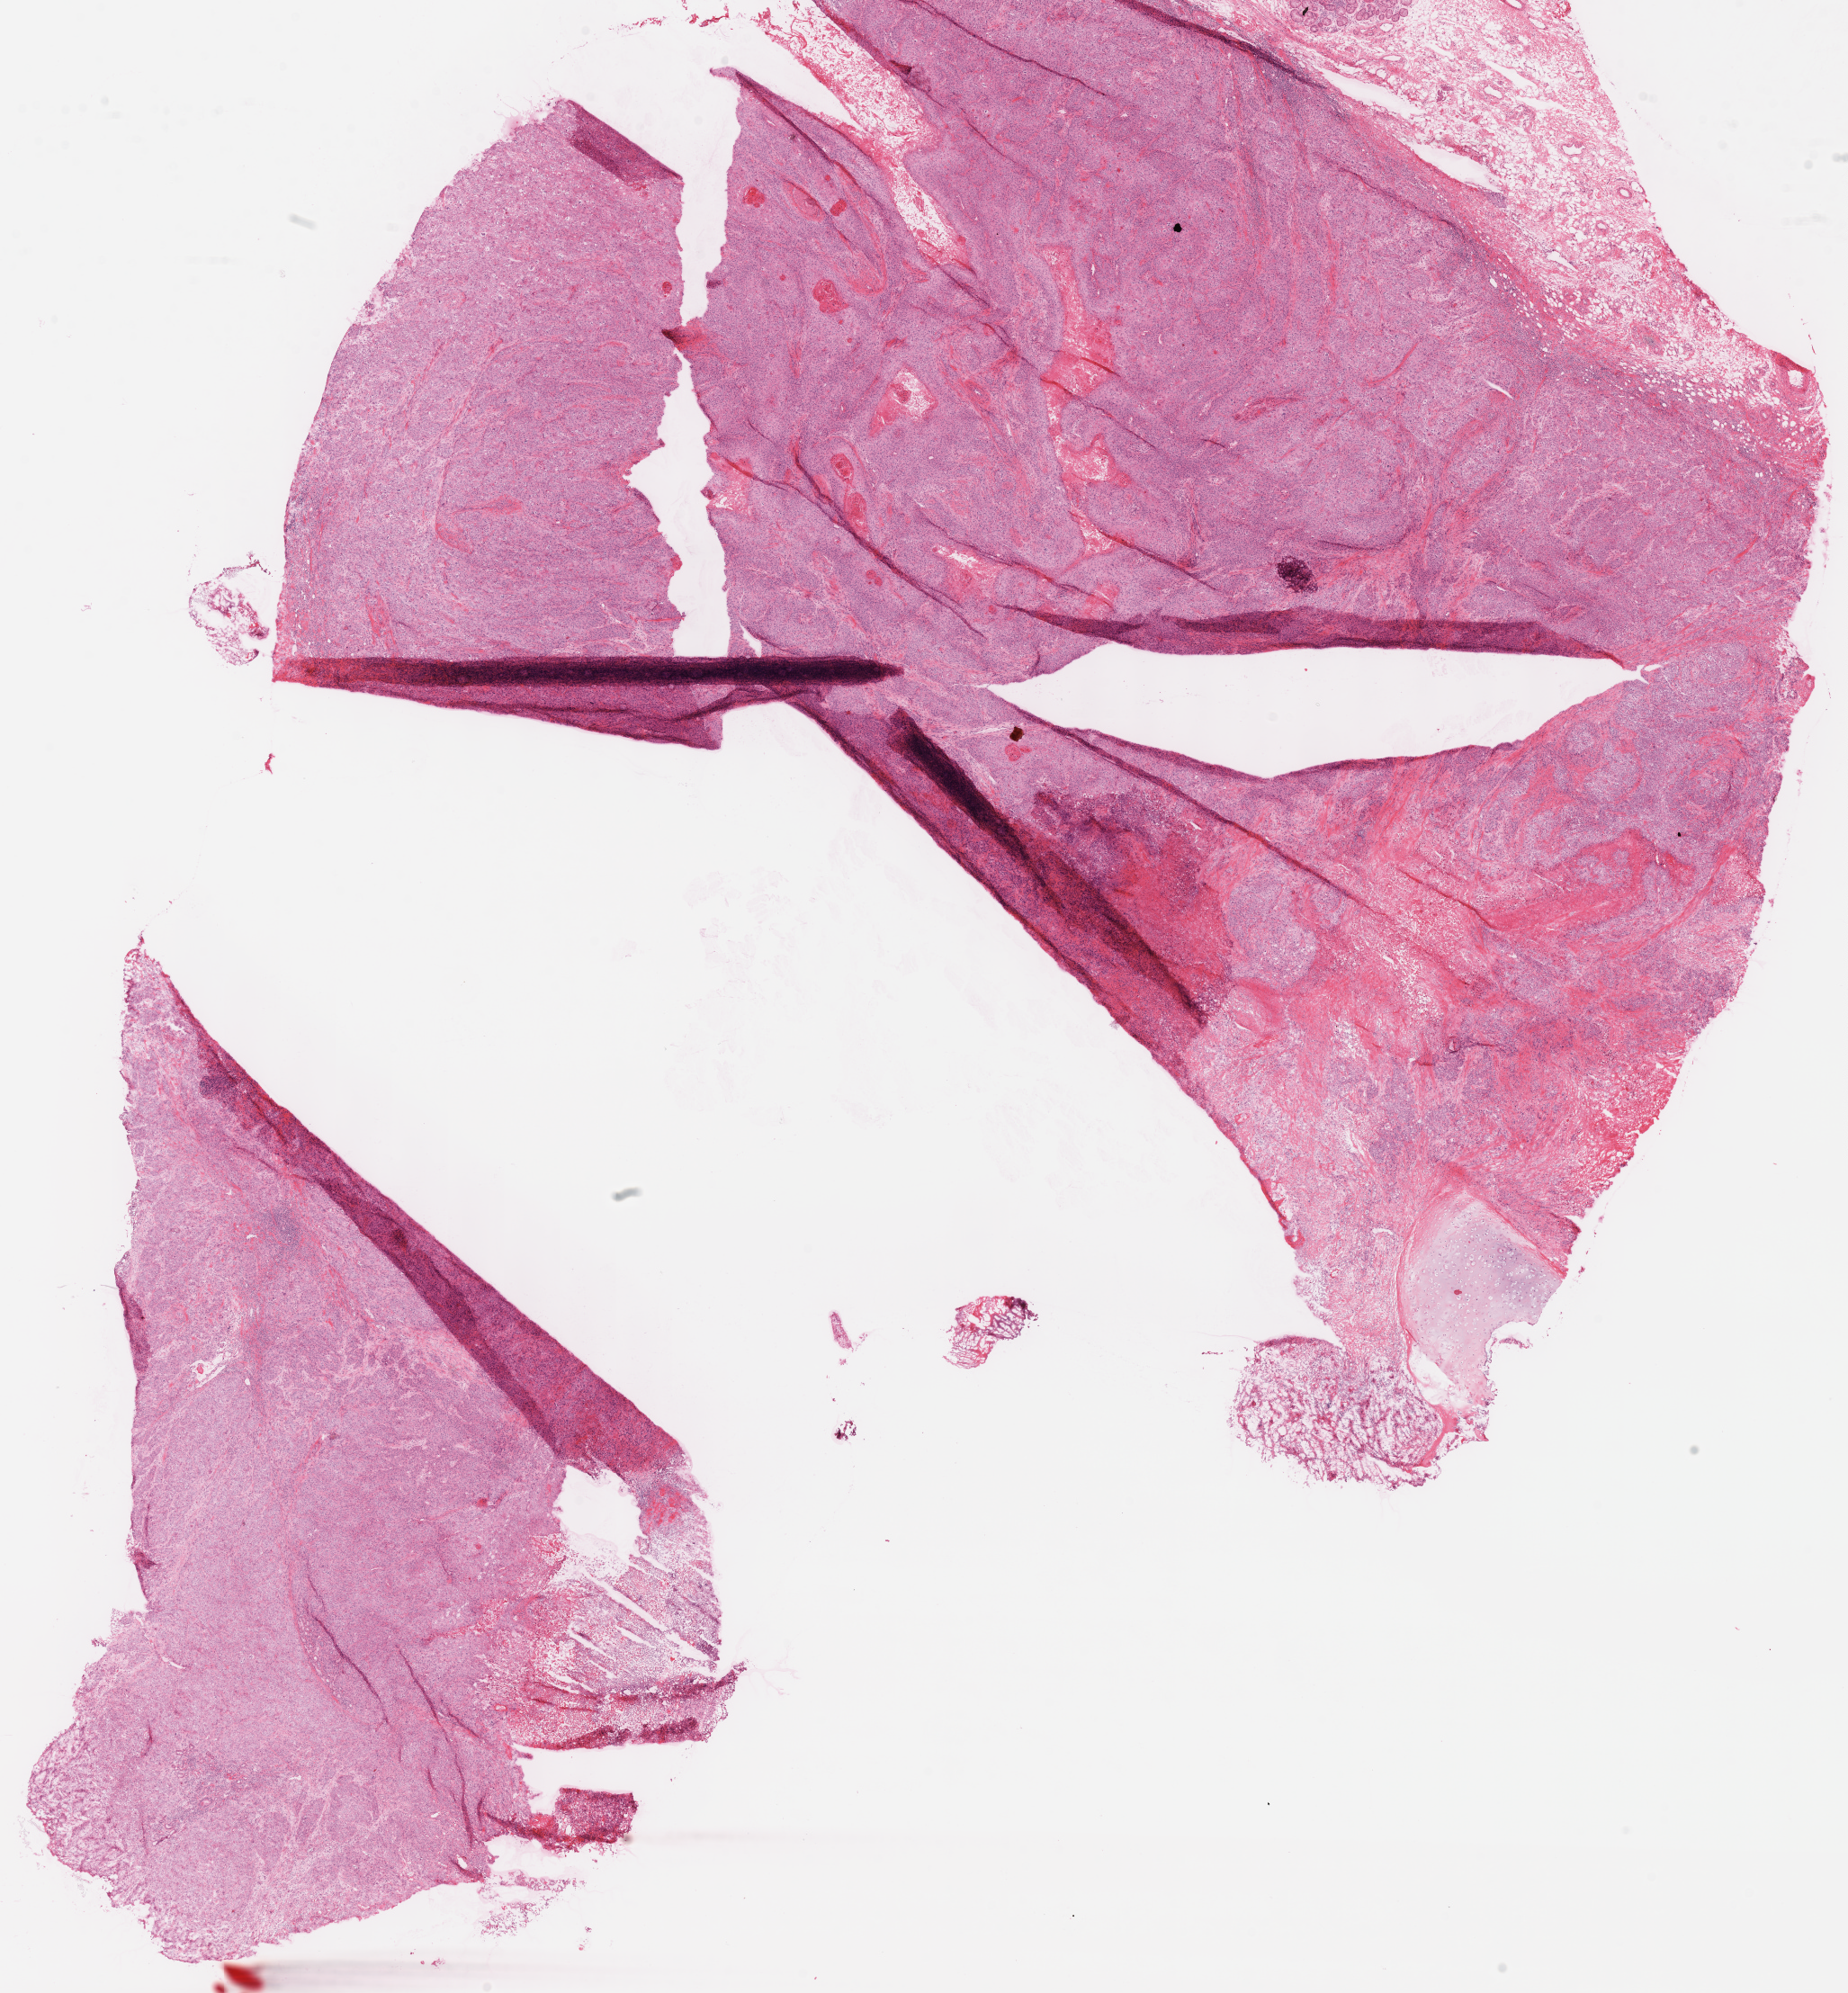
H&E-stained whole-slide image — a low-resolution overview of the entire scanned area, about 16.2 x 17.4 mm. Frozen section. Sample: primary tumour, head and neck. Patient: male, age at initial diagnosis 58 years. Histologic grade: G1 (well differentiated). Pathologist review of this section (percent, as recorded): tumour cells 80%, tumour nuclei 80%, normal cells 0%, stromal cells 20%, necrosis 0%.
AJCC pathologic stage: I. Histologic diagnosis: Squamous cell carcinoma, NOS.